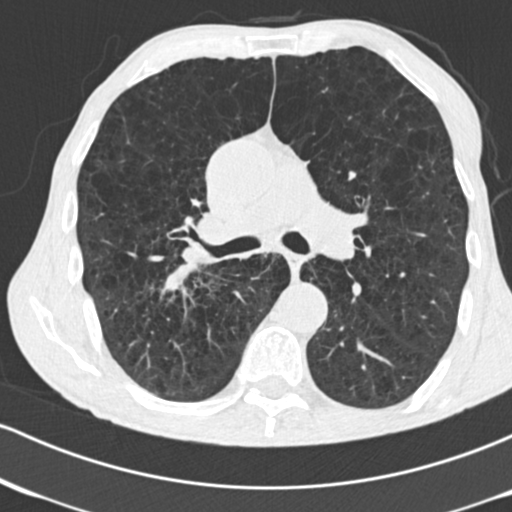
Low-dose screening chest CT, one axial slice; position 103 of 182 along the scan axis; reconstruction kernel B30f; lung window (W 1500 / L -600 HU); 512 × 512 image matrix, field of view 316 × 316 mm.
Annotated regions visible in this slice (manually delineated by an expert):
- lesion 1 (tumor, lower lobe of right lung): bounding box [x1, y1, x2, y2] px = [162, 263, 197, 292]